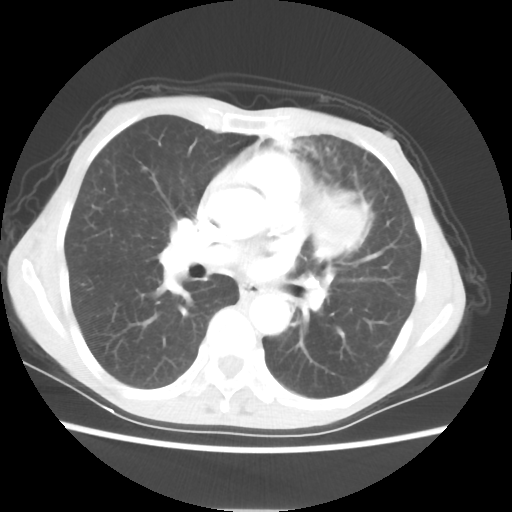
Chest CT, one axial slice; slice 31 of 56 in the series (ordered by position); 80 kVp; lung window (W 1500 / L -600 HU); 5 mm slice thickness; 512 × 512 image matrix, field of view 331 × 331 mm. Patient: female, 60 years. From the clinical record (not read from this slice): clinical TNM (as recorded): T4 N1 M0.
Outlined on this slice (bounding box drawn by a radiologist):
- lung tumour (recorded histology: adenocarcinoma): box from (x=308, y=186) to (x=365, y=256) px